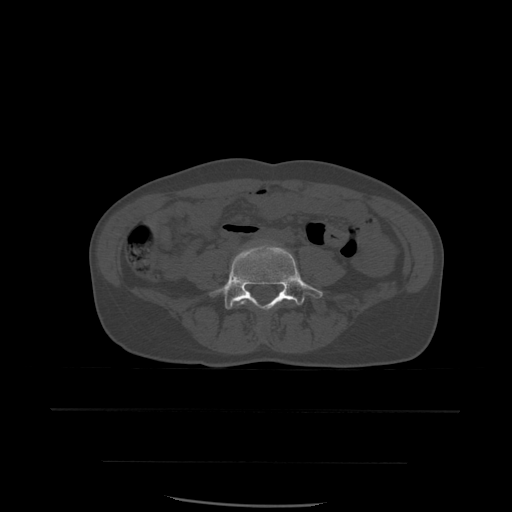
CT including the spine, one axial slice; position 155 of 574 along the scan axis; bone window (W 1800 / L 400 HU); 512 × 512 image matrix, field of view 392 × 392 mm. Patient age 48 years. From the clinical record (not read from this slice): primary cancer: lung; vertebrae with lytic lesions (as recorded): T11.
Outlined on this slice (semi-automatically segmented with operator editing):
- L4 vertebra: bounding box [x1, y1, x2, y2] px = [236, 294, 291, 326]
- L5 vertebra: [211, 246, 323, 310]